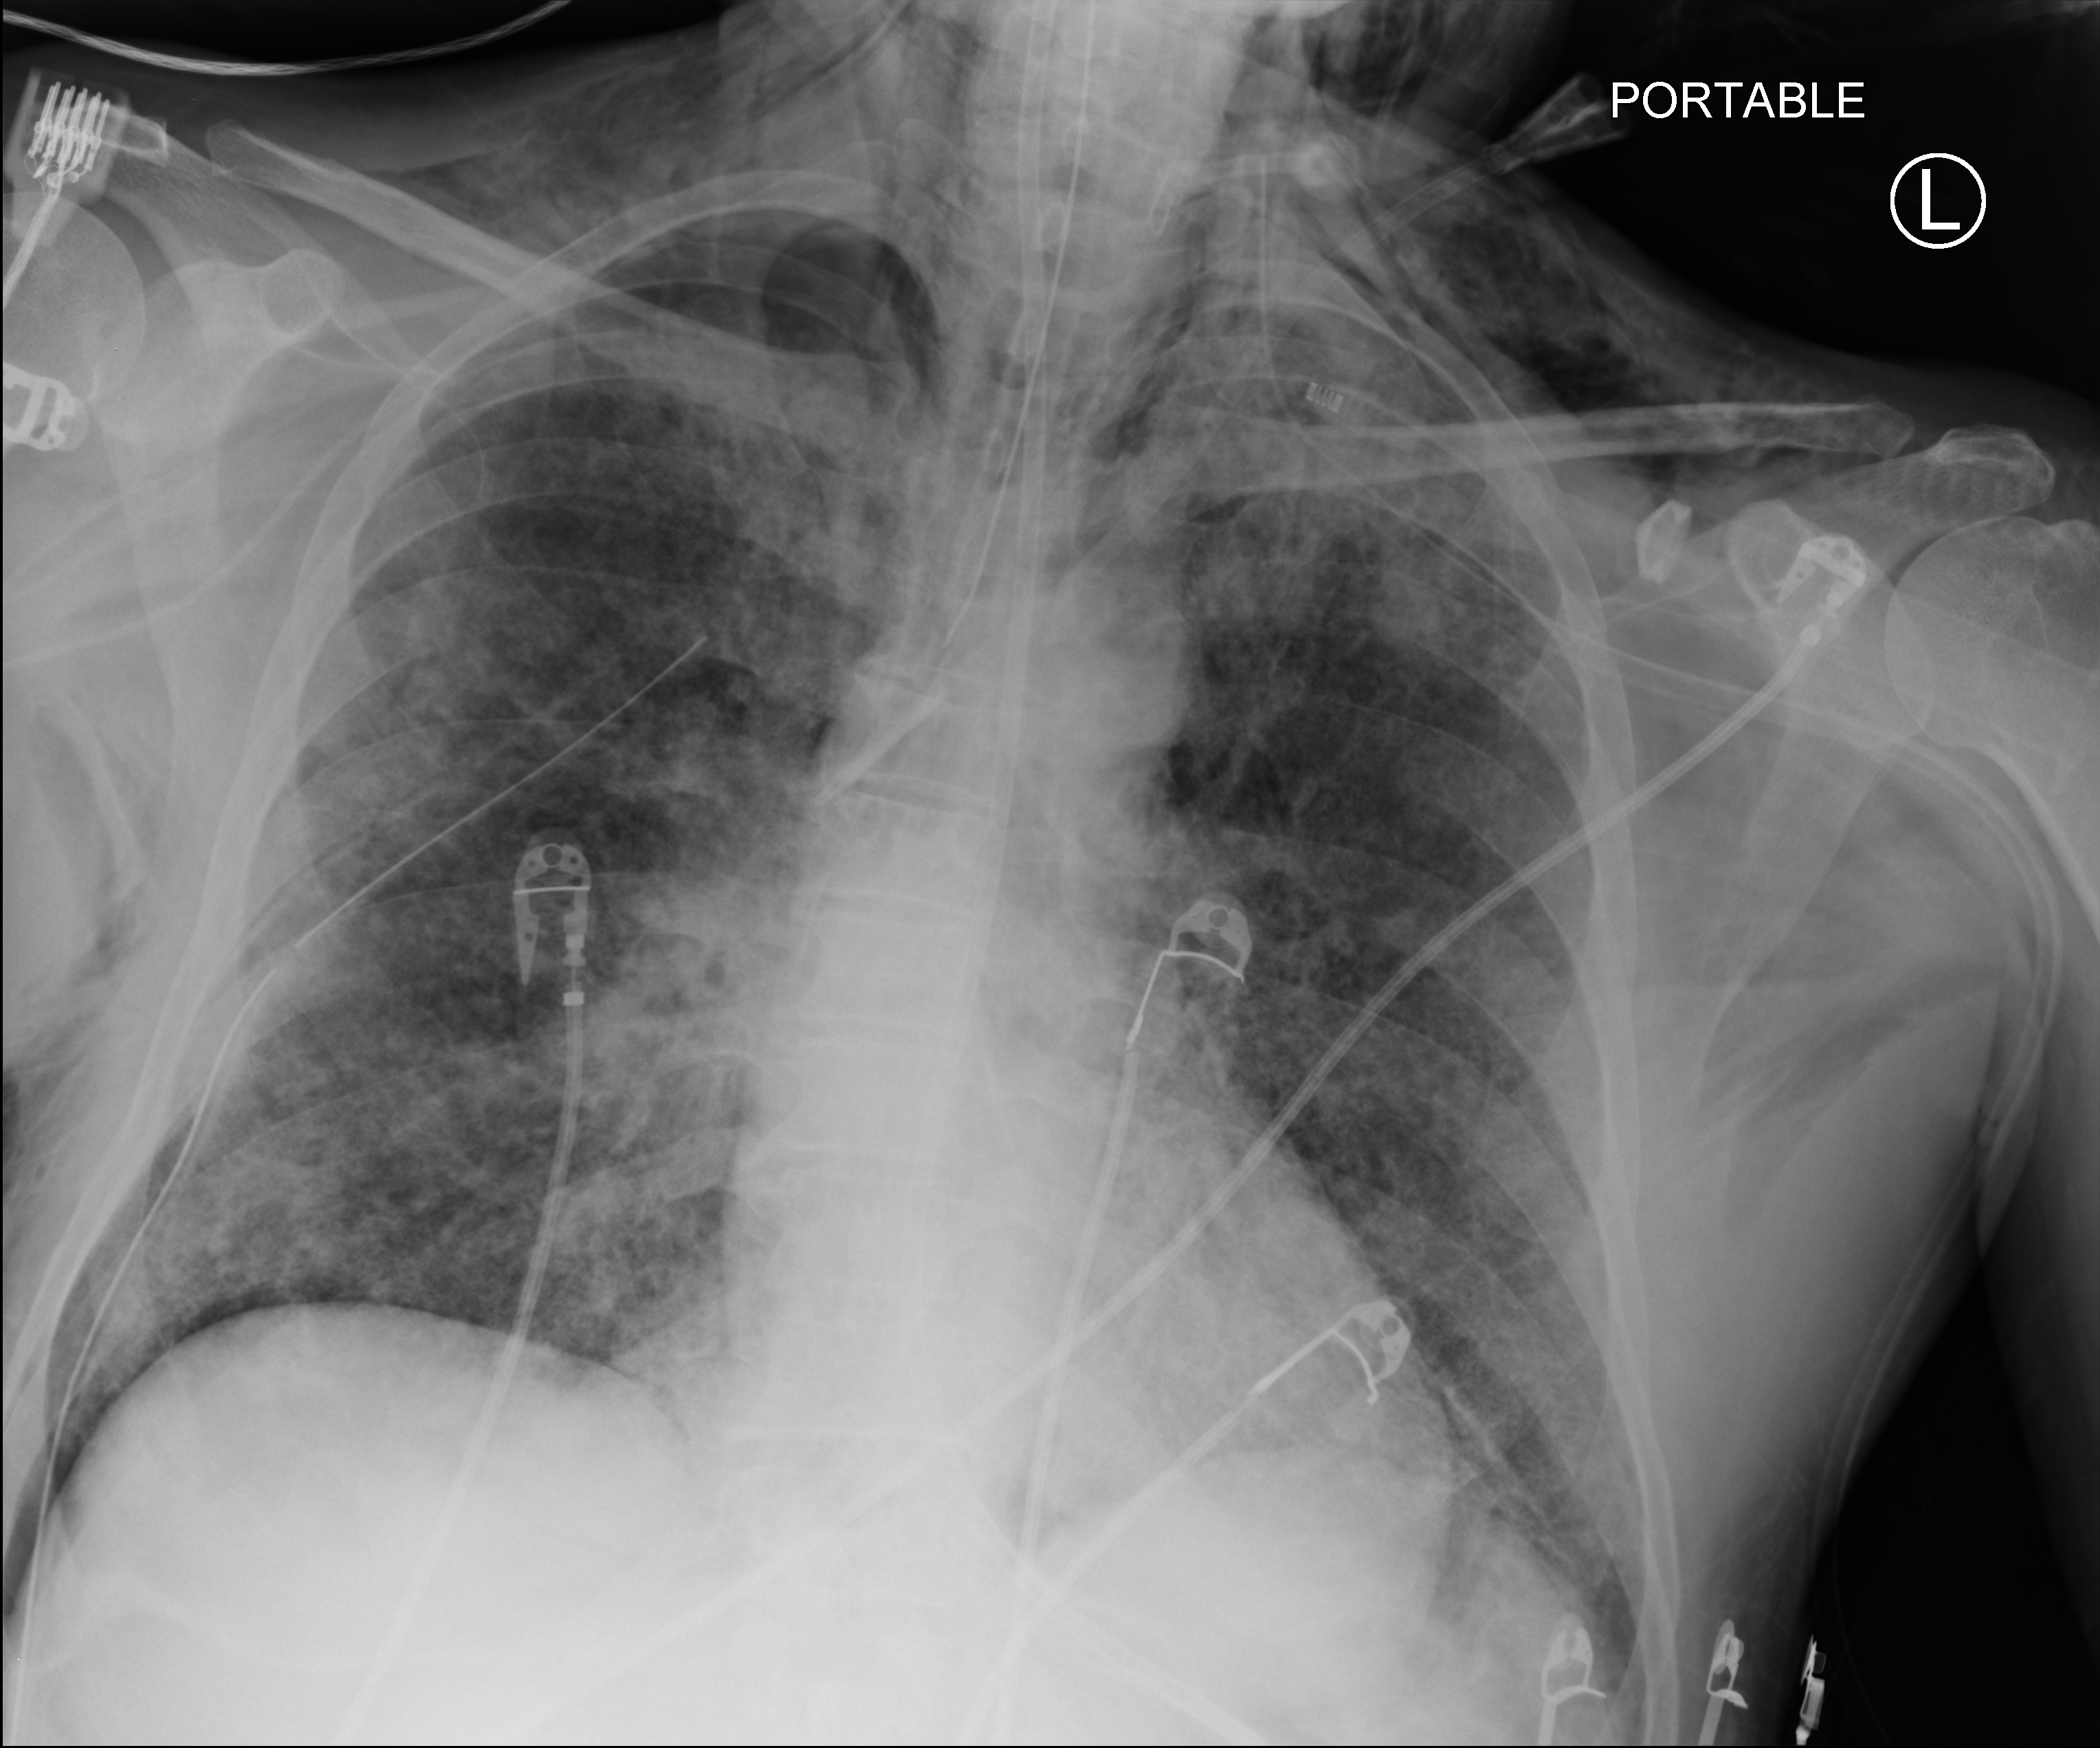
Bedside chest radiograph (computed radiography); anteroposterior (AP) projection. Male patient hospitalised with COVID-19, age 18–59 years.
Hospital-stay facts (about this admission, not read from this image; timing relative to this image not recorded):
- mechanically ventilated during this hospital stay: yes
- diabetes (admission record): no
- admitted to intensive care during this hospital stay: yes